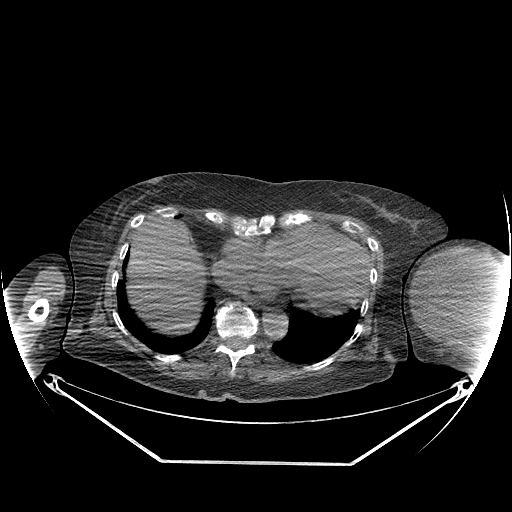
CT of an extremity soft-tissue mass (from a PET/CT study), one axial slice; slice 150 of 267 in the series (ordered by position); reconstruction kernel STANDARD; 140 kVp; soft-tissue window (W 400 / L 40 HU); 3.75 mm slice thickness; 512 × 512 image matrix, field of view 500 × 500 mm. Female patient. From the clinical record (not read from this slice): histological type: pleiomorphic leiomyosarcoma; grade: high; site of the primary tumour: left biceps.
Structures marked on this image (expert contour drawn on MRI and transferred to this co-registered scan by the dataset authors):
- gross tumour volume including surrounding oedema: bounding box <413,249,497,327> (left, top, right, bottom; pixels)
- gross tumour volume (mass): <413,249,497,327>